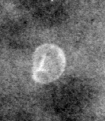
Region of interest cut from a scanned film mammogram (one marked finding); right breast; MLO view; BI-RADS breast density category 4 (scale 1–4).
Marked abnormality: calcifications, morphology lucent center; BI-RADS assessment category 2; benign without callback (not worked up further).